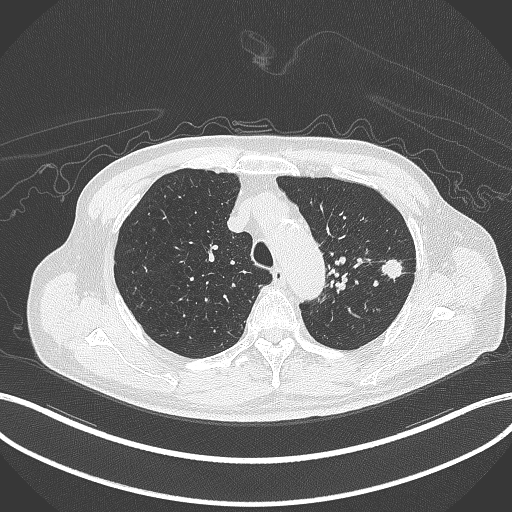
Chest CT, one axial slice. Position 340 of 417 along the scan axis. Reconstruction kernel B70f. Lung window (W 1500 / L -600 HU). 512 × 512 image matrix, field of view 400 × 400 mm. Patient: male, 77 years. Case-level facts recorded for this patient, not image findings: clinical TNM (as recorded): T3 N1 M0.
Outlined on this slice (bounding box drawn by a radiologist):
- lung tumour (recorded histology: adenocarcinoma): bounding box (x1, y1, x2, y2) in pixels: (381, 253, 402, 281)